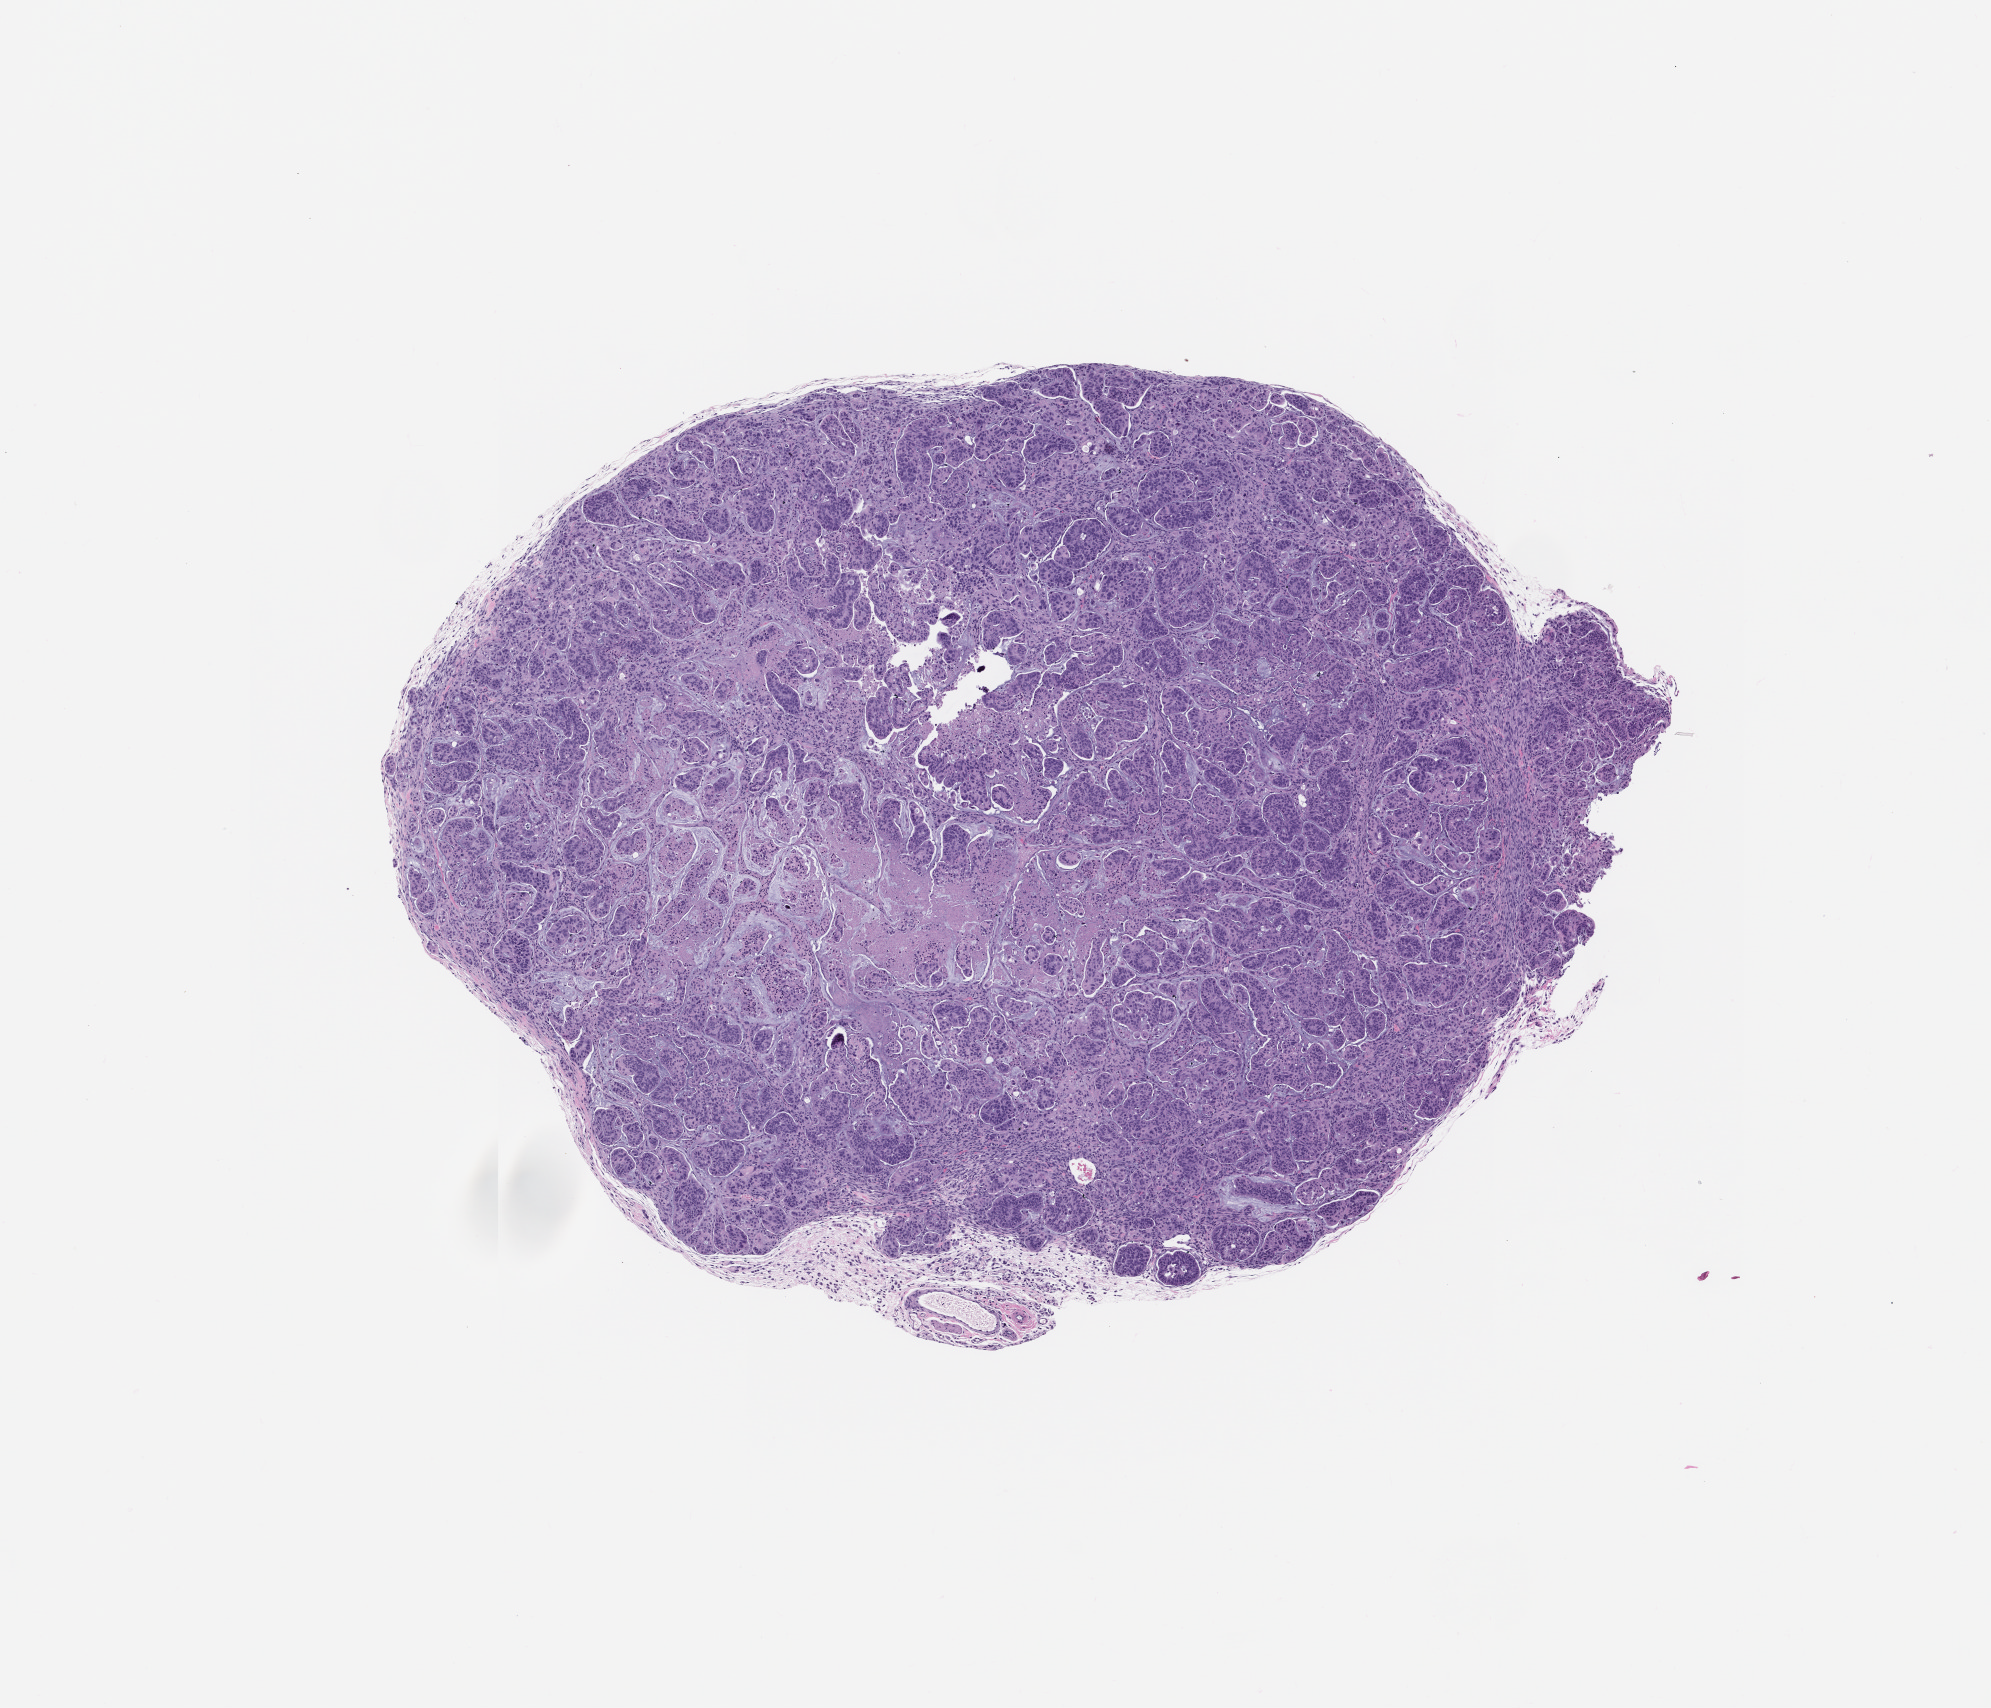
Whole-slide image, haematoxylin and eosin: patient-derived xenograft (human tumor grown in a mouse), passage 1, a low-resolution overview of the entire scanned area, about 8.0 x 6.8 mm, formalin-fixed paraffin-embedded section, tumor site category: small intestine.
* originating patient diagnosis: Small Intestinal Adenocarcinoma